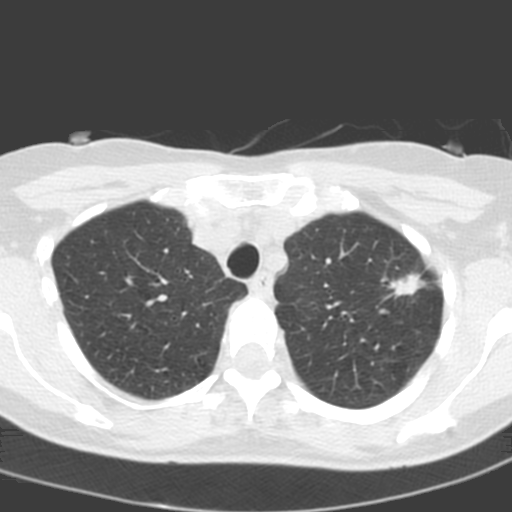
Axial slice from a low-dose chest CT screening exam, baseline screening round, lung window (W 1500 / L -600 HU), 3.2 mm slice thickness, standard (soft-tissue) reconstruction kernel (C), 120 kVp, slice 39 of 193 in the series, 512 × 512 image matrix, field of view 272 × 272 mm. Female, age 58 years at enrolment. Current smoker at enrolment.
Expert-annotated lung lesion, bounding box [x1, y1, x2, y2] px = [379, 264, 430, 315]. Reader record for this screening exam (exam-level; its link to the box is not recorded): non-calcified nodule or mass ≥4 mm, left upper lobe, 14 × 10 mm, spiculated (stellate) margins, soft tissue attenuation. Participant outcome: lung cancer diagnosed 48 days after this screen — adenocarcinoma, NOS, left upper lobe, poorly differentiated (G3), stage IA (AJCC 6th edition), 13 mm at pathology.